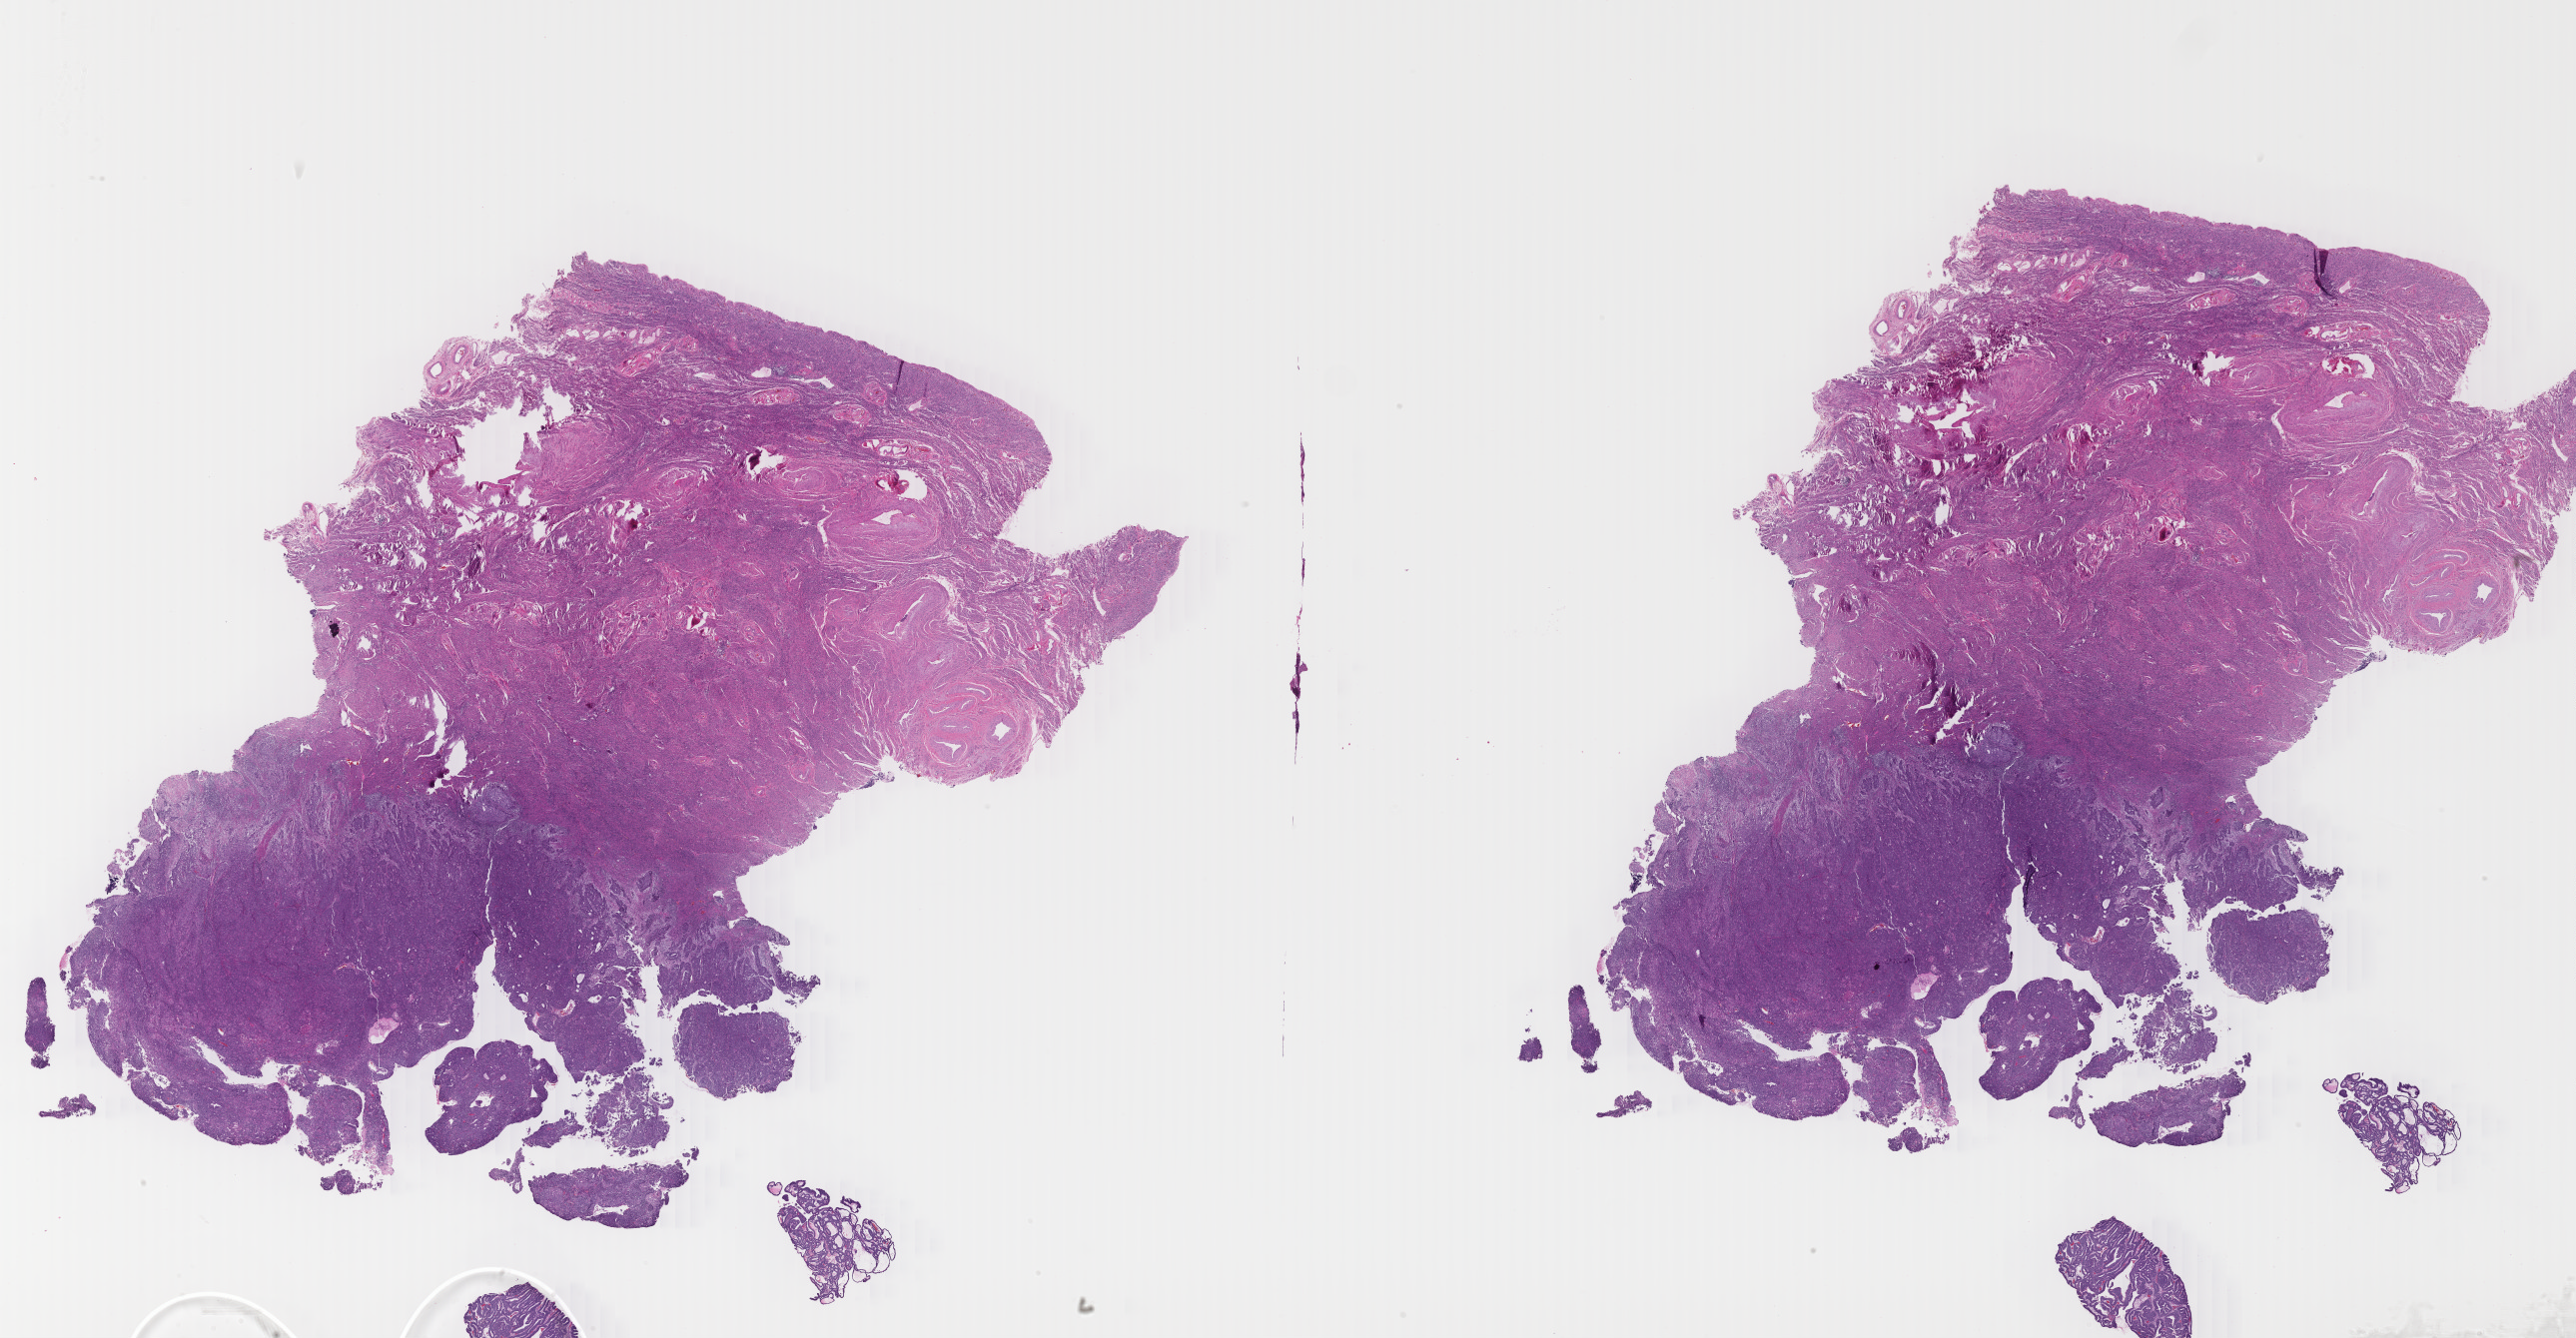
Digitized H&E tissue section (whole slide) — whole scanned area (about 41.5 x 21.5 mm, slide scanned at 40x) shown as a low-resolution overview; formalin-fixed paraffin-embedded (FFPE) diagnostic section; primary tumour sample from the uterus. Female patient; age at initial diagnosis 55 years. Histologic grade: G3 (poorly differentiated).
* FIGO stage: IA
* diagnosis: Endometrioid adenocarcinoma, NOS (endometrium)